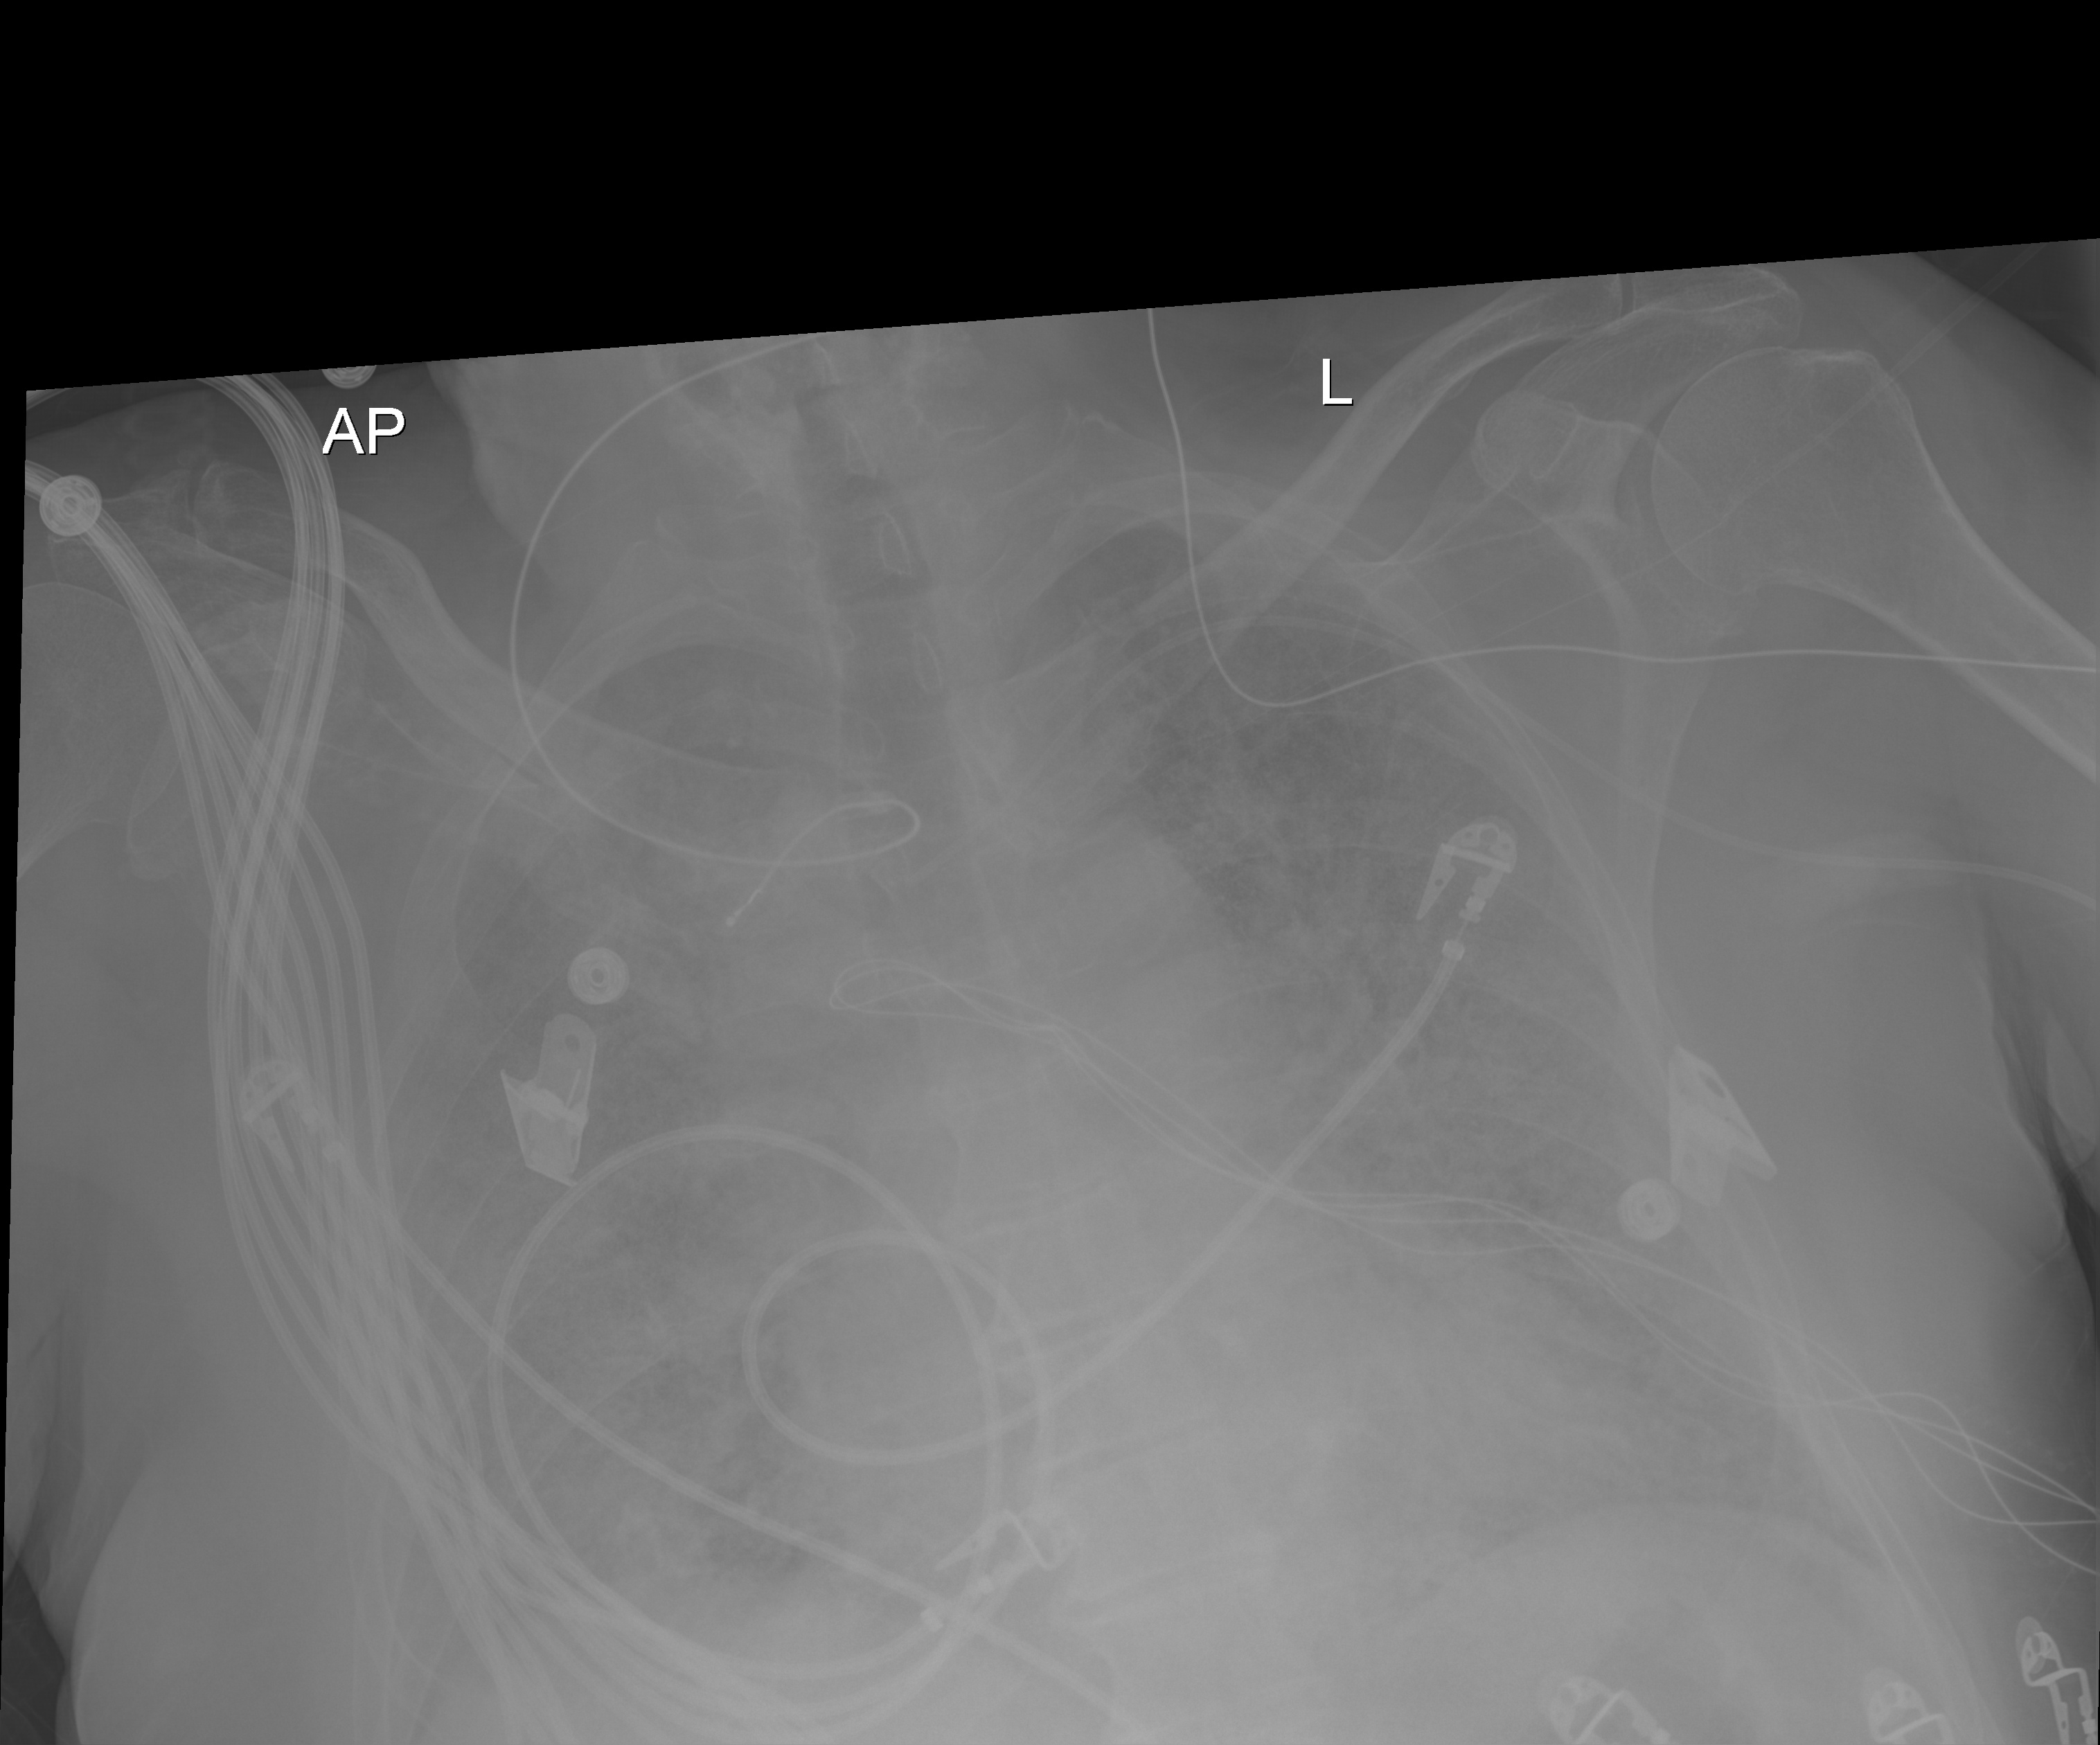
Chest X-ray (portable); anteroposterior (AP) projection. Patient hospitalised with COVID-19; male, aged 75–90 years.
Hospital-stay facts (about this admission, not read from this image; timing relative to this image not recorded):
- mechanically ventilated during this hospital stay: yes
- admitted to intensive care during this hospital stay: yes
- diabetes (admission record): no